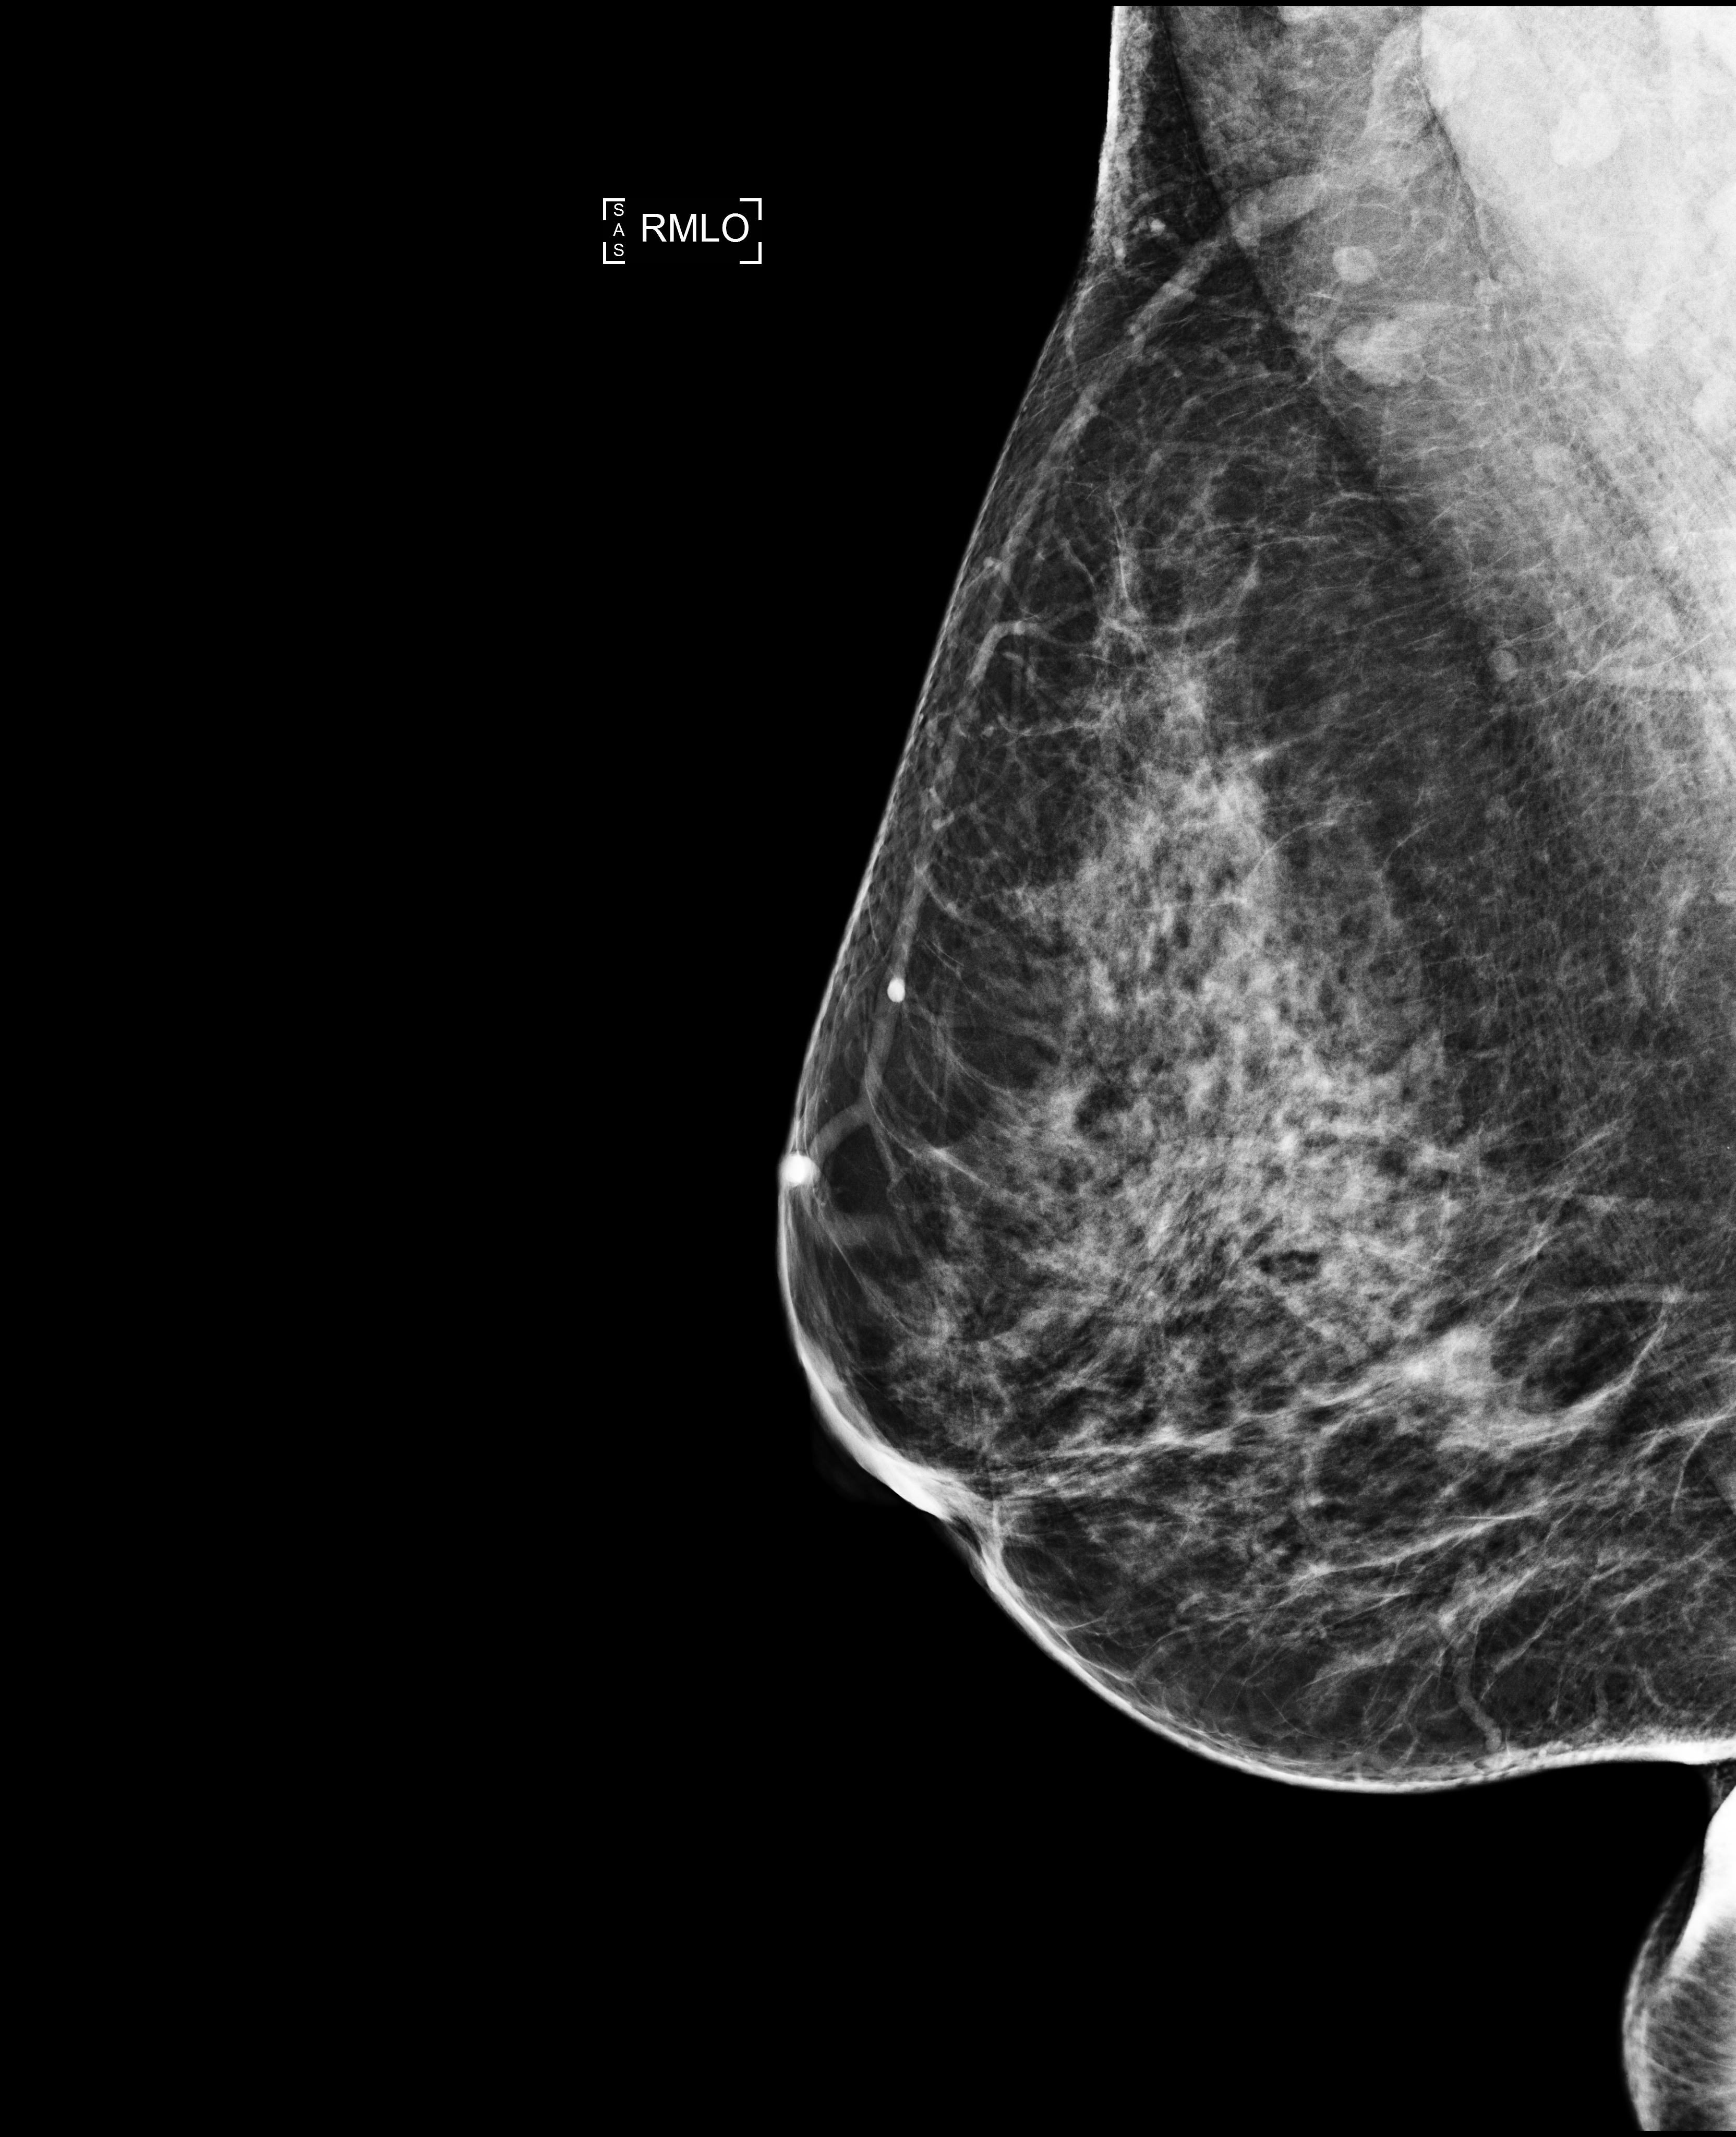
Screening examination; compressed breast thickness 63 mm. Female patient, age 45 years.
Image type: full-field digital mammogram. Breast: right. Projection: MLO view.